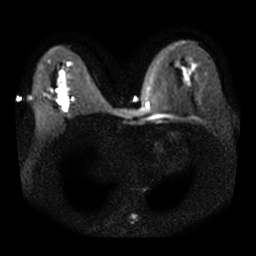
Breast MRI, one axial slice. Slice 17 of 31 in the series (ordered by position). Diffusion-weighted series; image 2 of 4 stored at this slice position (different b-values; order by instance number). 3 T. 256 × 256 image matrix. Female patient.
Annotated regions visible in this slice (outlined manually by an expert reader):
- tumour on diffusion-weighted imaging: box from (x=60, y=95) to (x=68, y=111) px